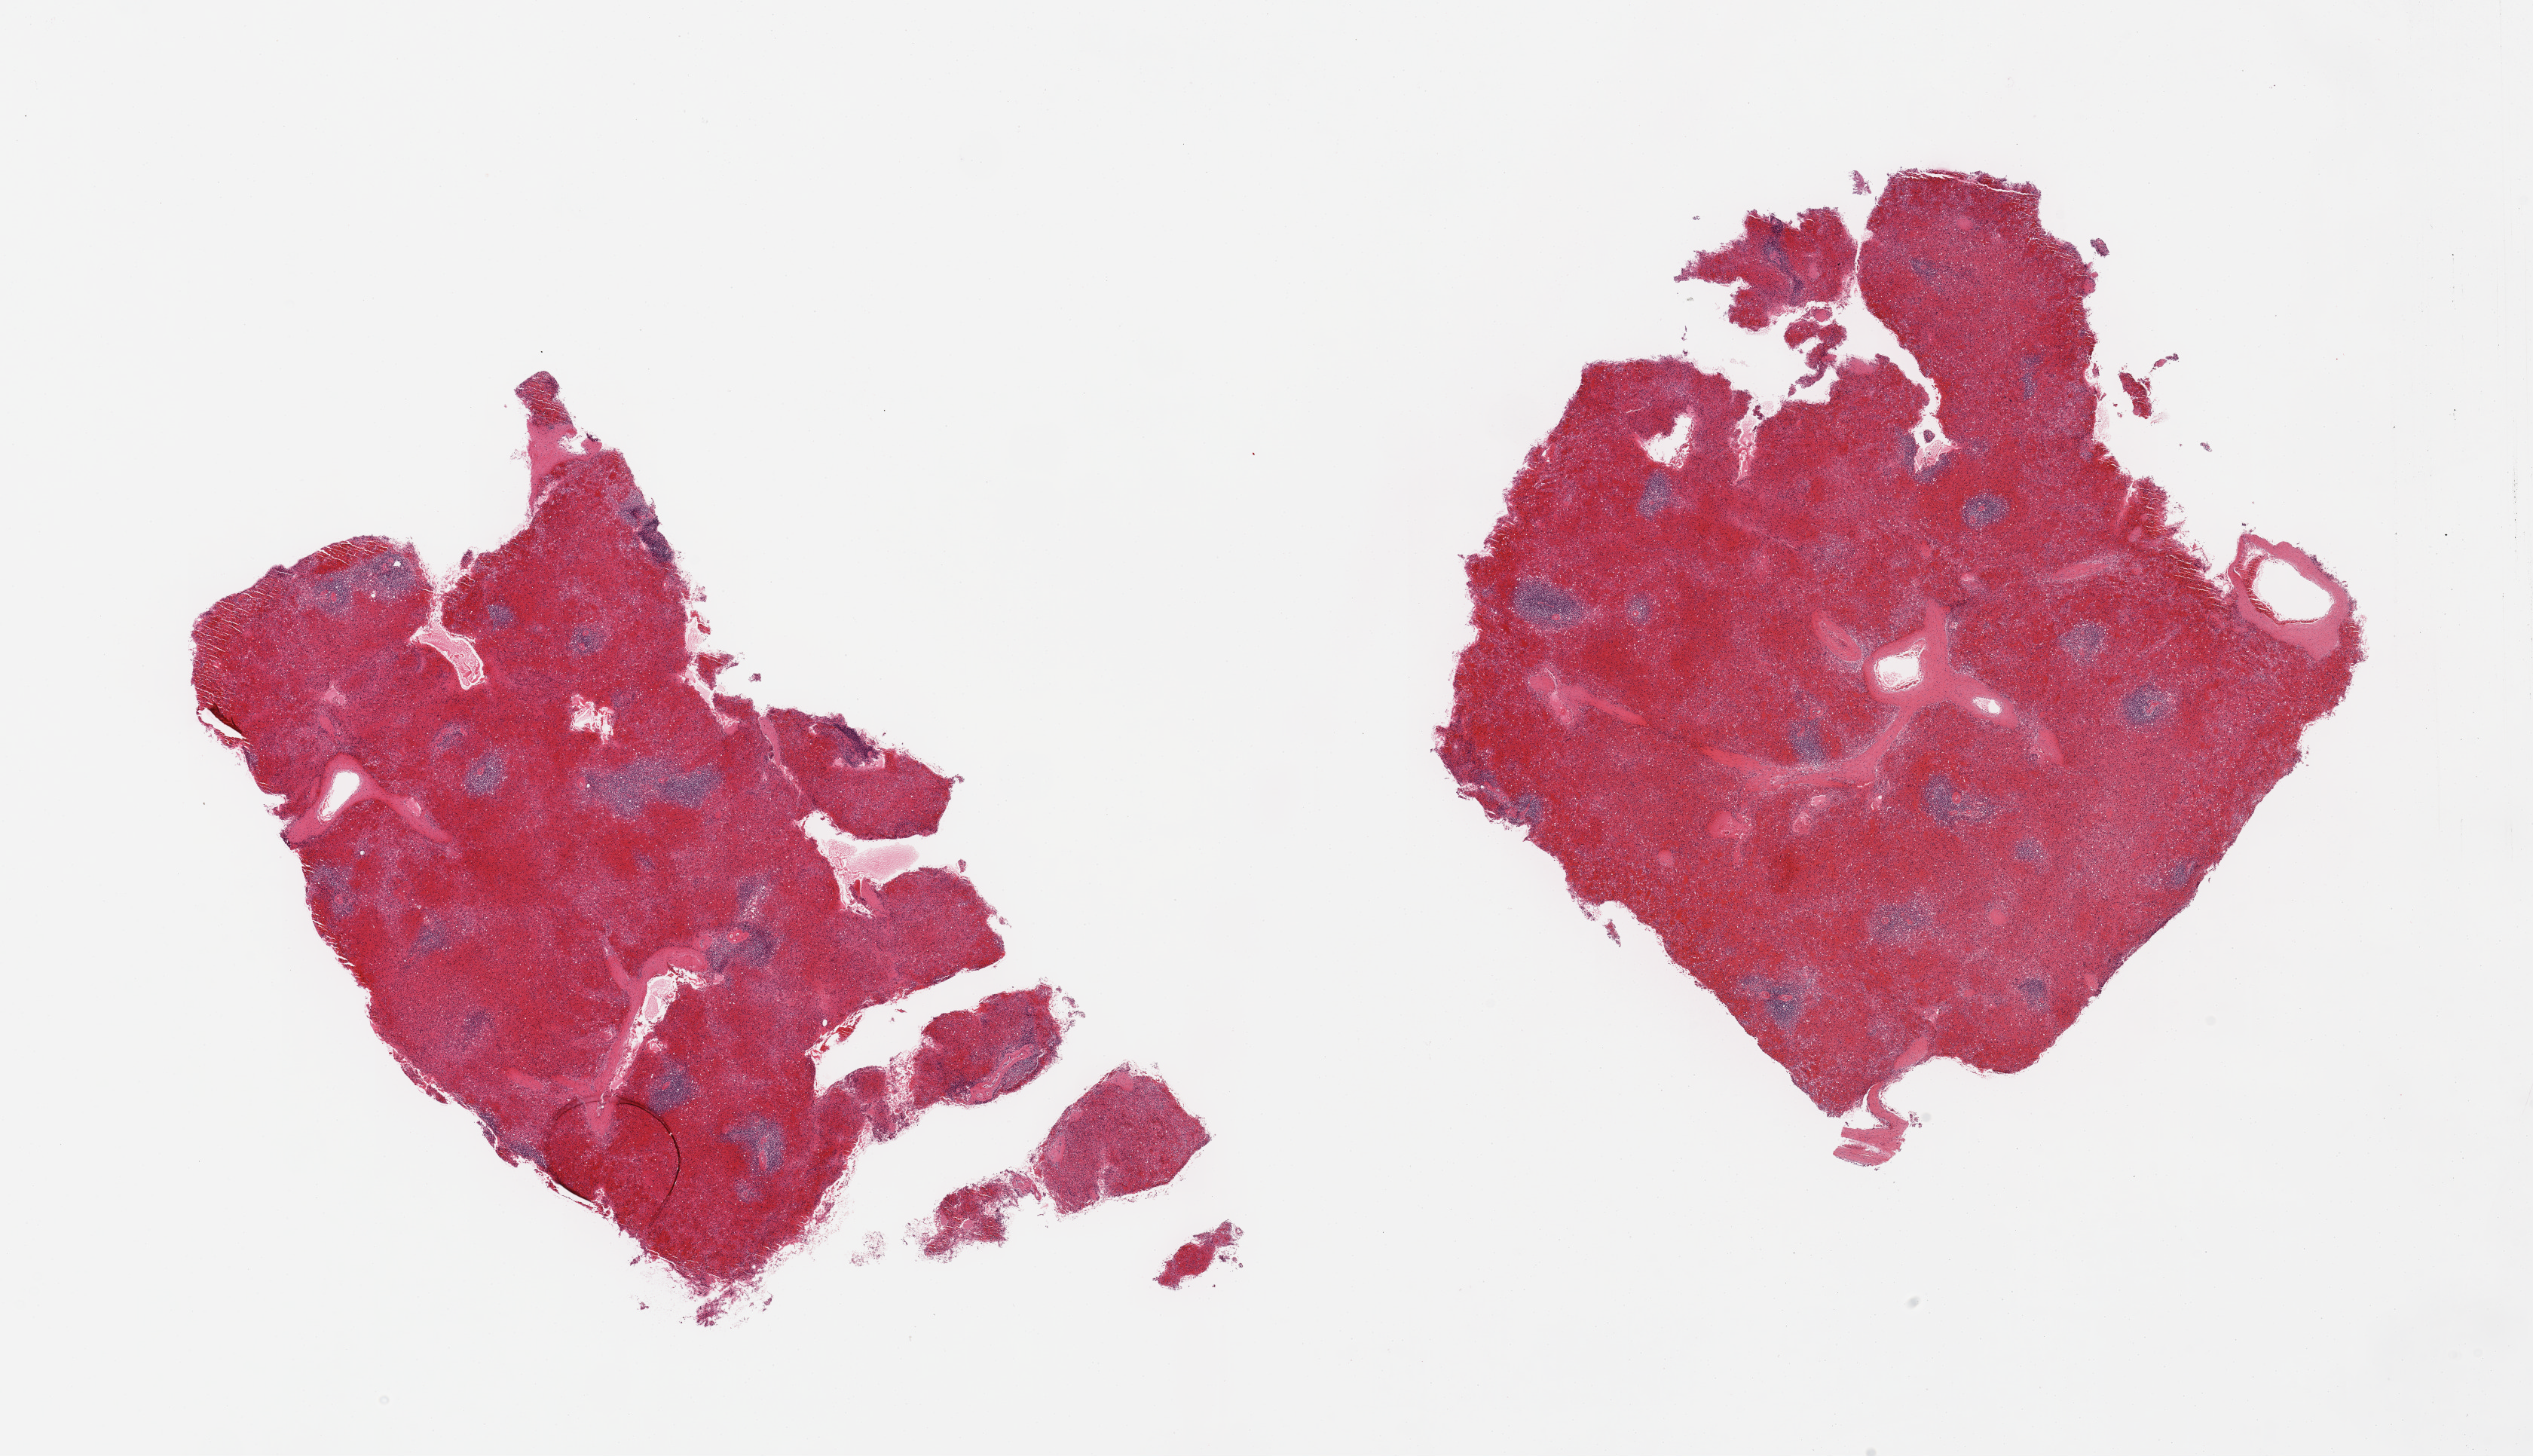
Digitized H&E-stained section, brightfield, low-resolution overview of the scanned area, about 26.6 x 15.3 mm. PAXgene-fixed, paraffin-embedded tissue. Sampled site (target tissue): spleen. Tissue donor sample. Donor sex: male.
• review note (as recorded): 2 pieces; congested